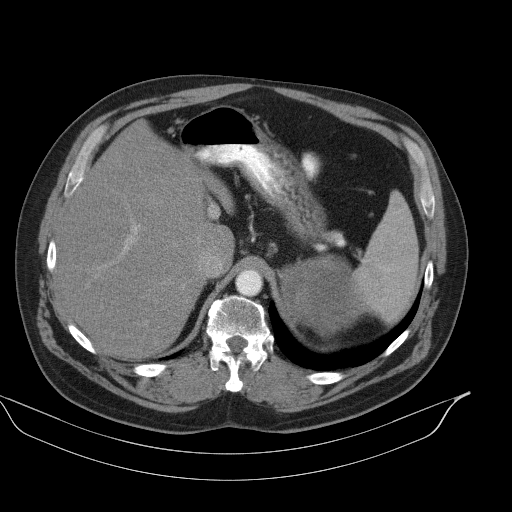
Contrast-enhanced abdominal CT, one axial slice. Slice 74 of 92 in the series (ordered by position). Soft-tissue window (W 400 / L 40 HU). 512 × 512 image matrix, field of view 449 × 449 mm. Male patient, age 56 years. Case-level facts recorded for this patient, not image findings: diagnosis: adrenocortical carcinoma; tumour side: left adrenal; tumour size at pathology: 15 cm; Ki-67 index: 35 %; stage (as recorded): 4.
Outlined on this slice (semi-automatic segmentation, software-assisted and operator-edited):
- mass: bounding box <281,257,372,336> (left, top, right, bottom; pixels)